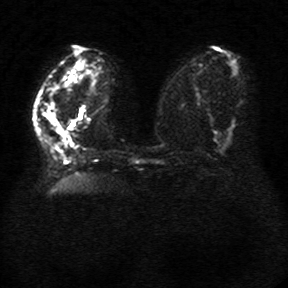
Breast MRI, one axial slice. Position 14 of 34 along the scan axis. Diffusion-weighted series; image 2 of 4 stored at this slice position (different b-values; order by instance number). 1.5 T. 5 mm slice thickness. 288 × 288 image matrix, field of view 340 × 340 mm. Female patient.
Annotated regions visible in this slice (manually delineated by an expert):
- tumour on diffusion-weighted imaging: bounding box [x1, y1, x2, y2] px = [42, 102, 63, 136]